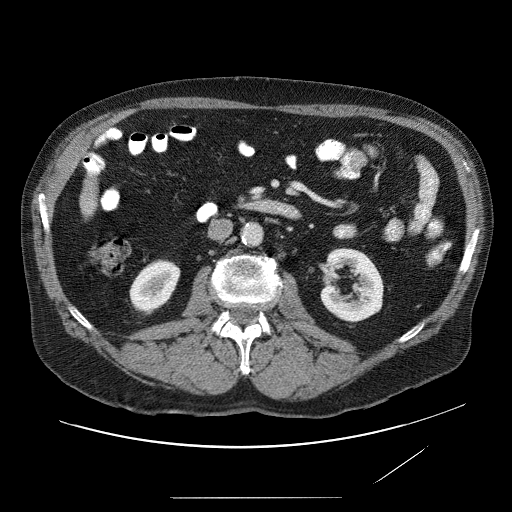
Contrast-enhanced abdominal CT (liver protocol), one axial slice; reconstruction kernel STANDARD; soft-tissue window (W 400 / L 40 HU); 512 × 512 image matrix. From the clinical record (not read from this slice): diagnosis: hepatocellular carcinoma (patient treated with transarterial chemoembolisation; whether this scan precedes or follows treatment is not stated here); TNM stage (as recorded): Stage-IVA; Child-Pugh class: A; tumour differentiation: moderately differentiated; tumour nodularity: multinodular.
Outlined on this slice (semi-automatically segmented with operator editing):
- liver parenchyma outside the tumour (the mass and vessels are separate outlines, so this box may not span the whole liver): bounding box <76,155,106,228> (left, top, right, bottom; pixels)